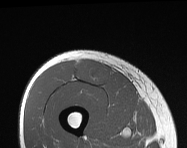
MRI of an extremity soft-tissue mass, one axial slice. Position 51 of 114 along the scan axis. MR volume resampled by the dataset authors to the PET/CT grid (not the native acquisition matrix). 187 × 148 image matrix. Male patient. Case-level facts recorded for this patient, not image findings: histological type: pleiomorphic leiomyosarcoma; grade: intermediate; site of the primary tumour: right thigh.
Annotated regions visible in this slice (expert contour drawn on MRI and transferred to this co-registered scan by the dataset authors):
- gross tumour volume including surrounding oedema: box from (x=75, y=59) to (x=112, y=87) px